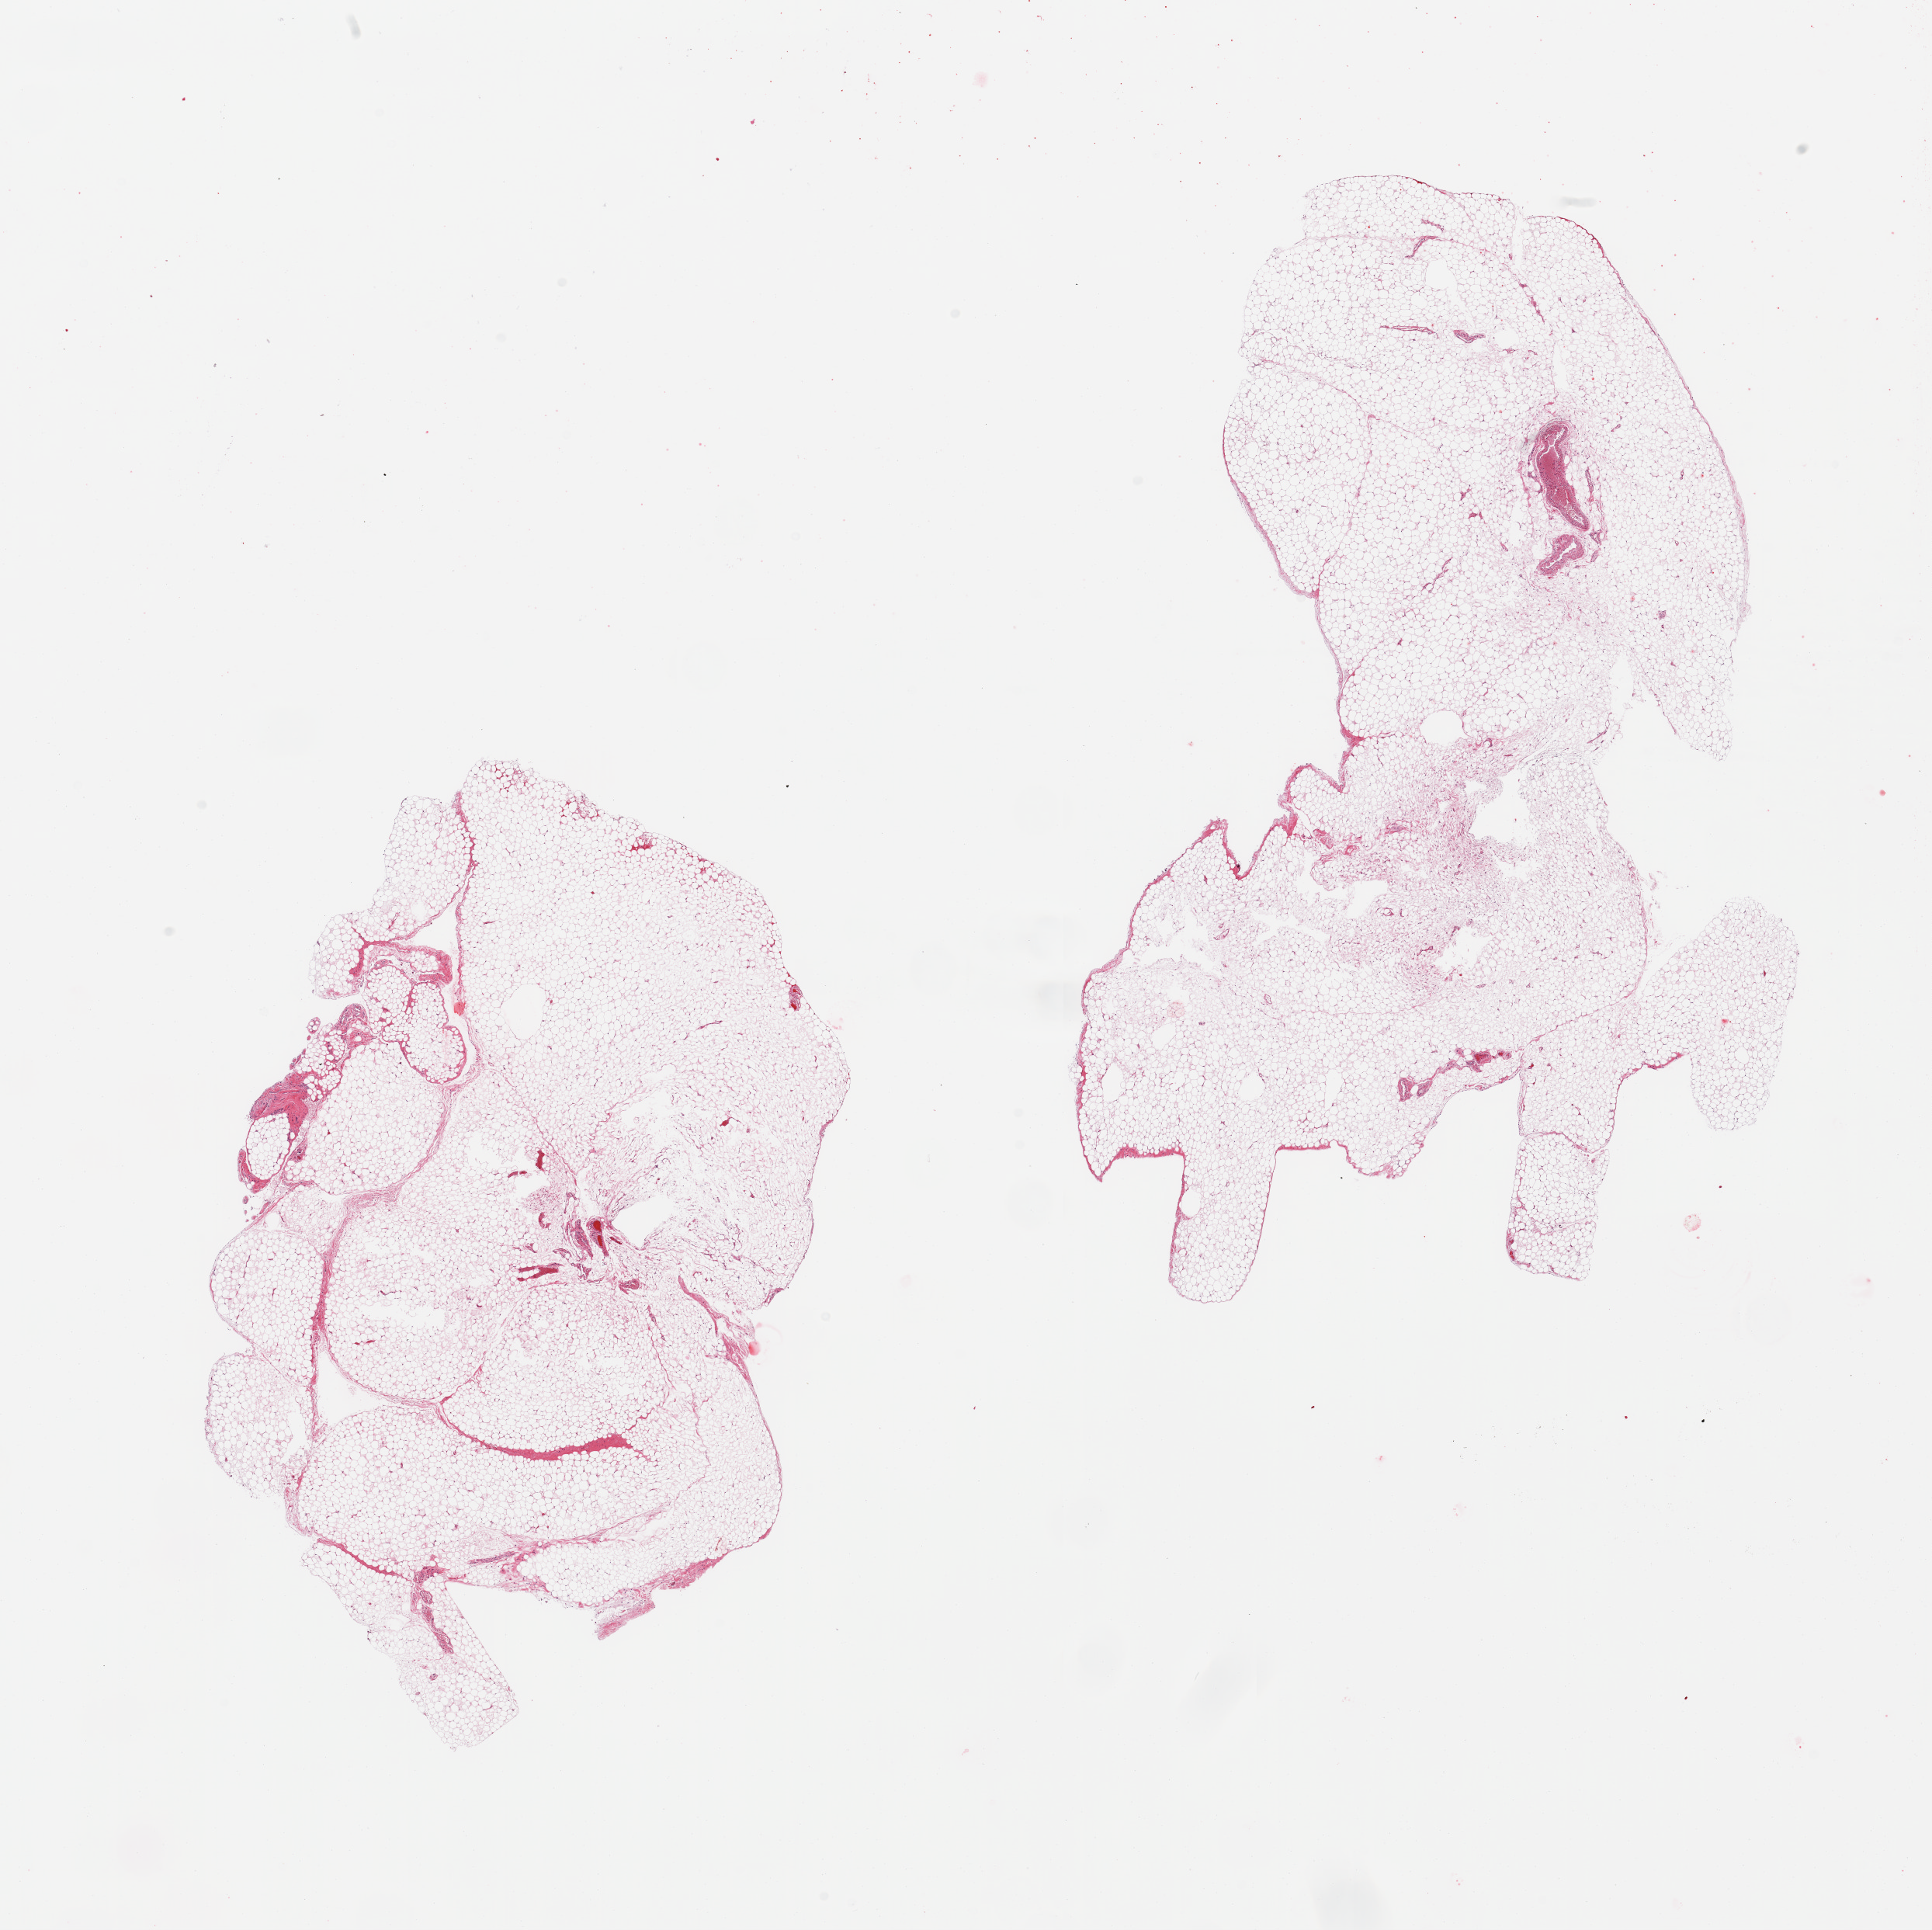
Whole-slide image, H&E stain, brightfield — a low-resolution overview of the entire scanned area, about 19.7 x 19.7 mm. PAXgene-fixed, paraffin-embedded tissue. Section of omentum (target tissue). Donor tissue sample.
- pathologist's review note for this sample: 2 pieces, ~5% vascular/fascia elements